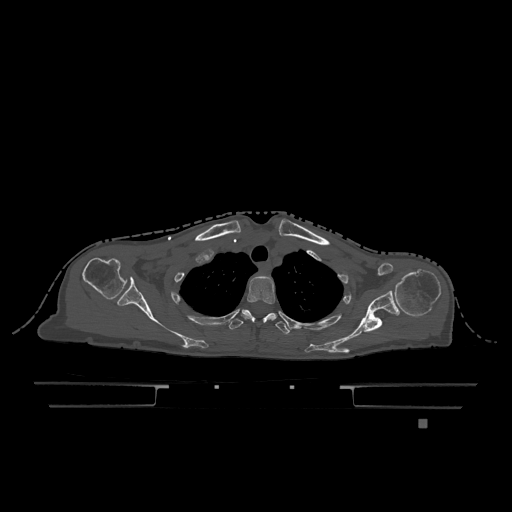
CT including the spine, one axial slice; bone window (W 1800 / L 400 HU); 512 × 512 image matrix. Patient: female, 74 years. From the clinical record (not read from this slice): primary cancer: lung; vertebrae with lytic lesions (as recorded): T1, T4, T5, T6, L4, L5.
Structures marked on this image (semi-automatically segmented with operator editing):
- T2 vertebra: bounding box (x1, y1, x2, y2) in pixels: (241, 276, 275, 320)
- T3 vertebra: (229, 310, 290, 335)
- T6 vertebra: (266, 313, 276, 318)